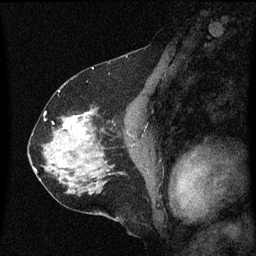
Breast MRI (dynamic contrast-enhanced), one sagittal slice; slice 34 of 60 in the series (ordered by position); dynamic contrast-enhanced series, image 2 of 3 at this slice position (ordered by acquisition); 1.5 T; TE 4.2 ms, TR 8 ms; 2 mm slice thickness; 256 × 256 image matrix. Female patient, age 58 years.
Structures marked on this image (semi-automatic segmentation, software-assisted and operator-edited):
- analysis volume of interest (the breast-tissue region the enhancement analysis was run in; not a lesion): bounding box <56,110,99,149> (left, top, right, bottom; pixels)
- tumour enhancement mask (voxels above the 70 % enhancement threshold inside the analysis volume of interest): <64,114,90,137>